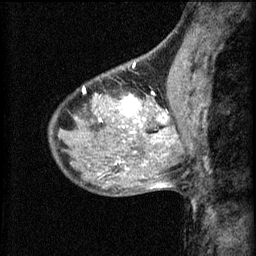
Breast MRI (dynamic contrast-enhanced), one sagittal slice; slice 25 of 60 in the series (ordered by position); 3 images stored at this slice position (order not interpretable as contrast timing); 1.5 T; TE 4.2 ms, TR 8.2 ms; 256 × 256 image matrix. Female patient, age 40 years.
Annotated regions visible in this slice (semi-automatic segmentation, software-assisted and operator-edited):
- analysis volume of interest (the breast-tissue region the enhancement analysis was run in; not a lesion): box from (x=108, y=82) to (x=175, y=139) px
- tumour enhancement mask (voxels above the 70 % enhancement threshold inside the analysis volume of interest): (x=116, y=94)–(x=169, y=135)